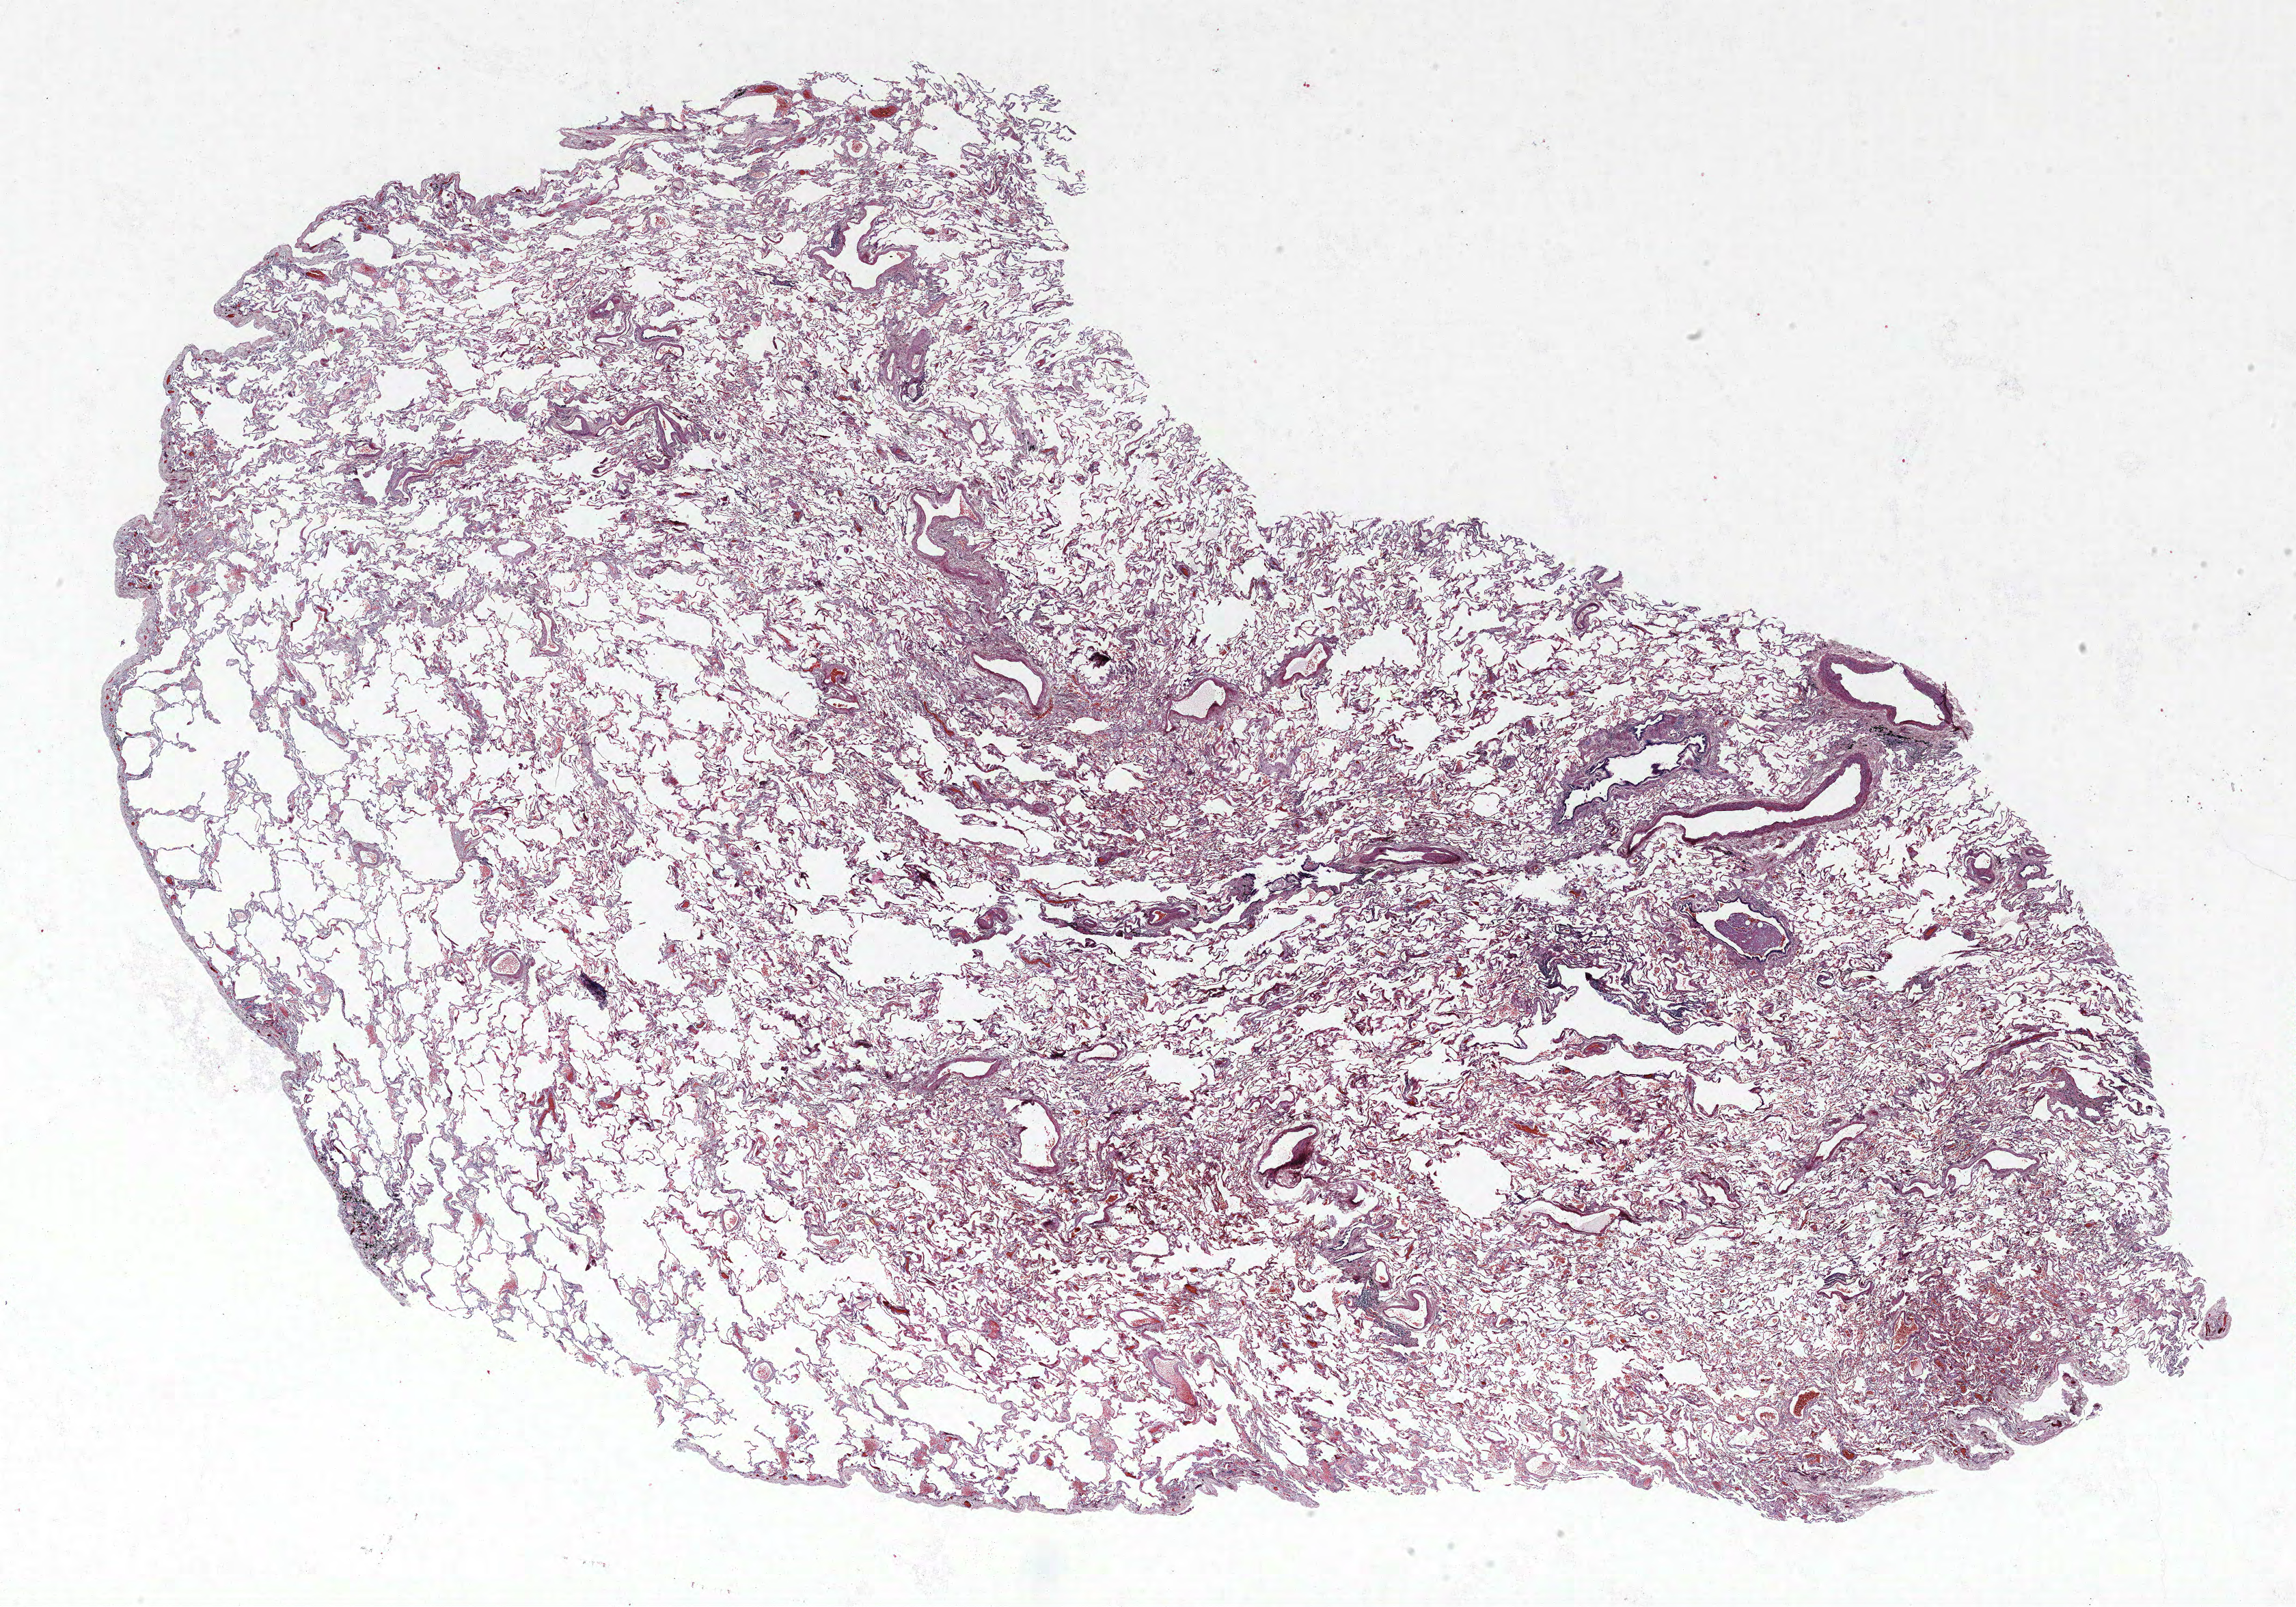
Whole-slide histology image, Hematoxylin and eosin (H&E) stained, whole scanned area (about 26.9 x 18.8 mm) shown as a low-resolution overview. FFPE section. Lung. Male, age 70 at enrolment. Former smoker at enrolment. Grade: moderately differentiated (G2).
* primary tumour location (clinical record): left upper lobe
* stage (AJCC 6th edition): IA
* tumour size (pathology): 20 mm
* participant's lung-cancer diagnosis: Mucin-producing adenocarcinoma (ICD-O-3 8481/3)